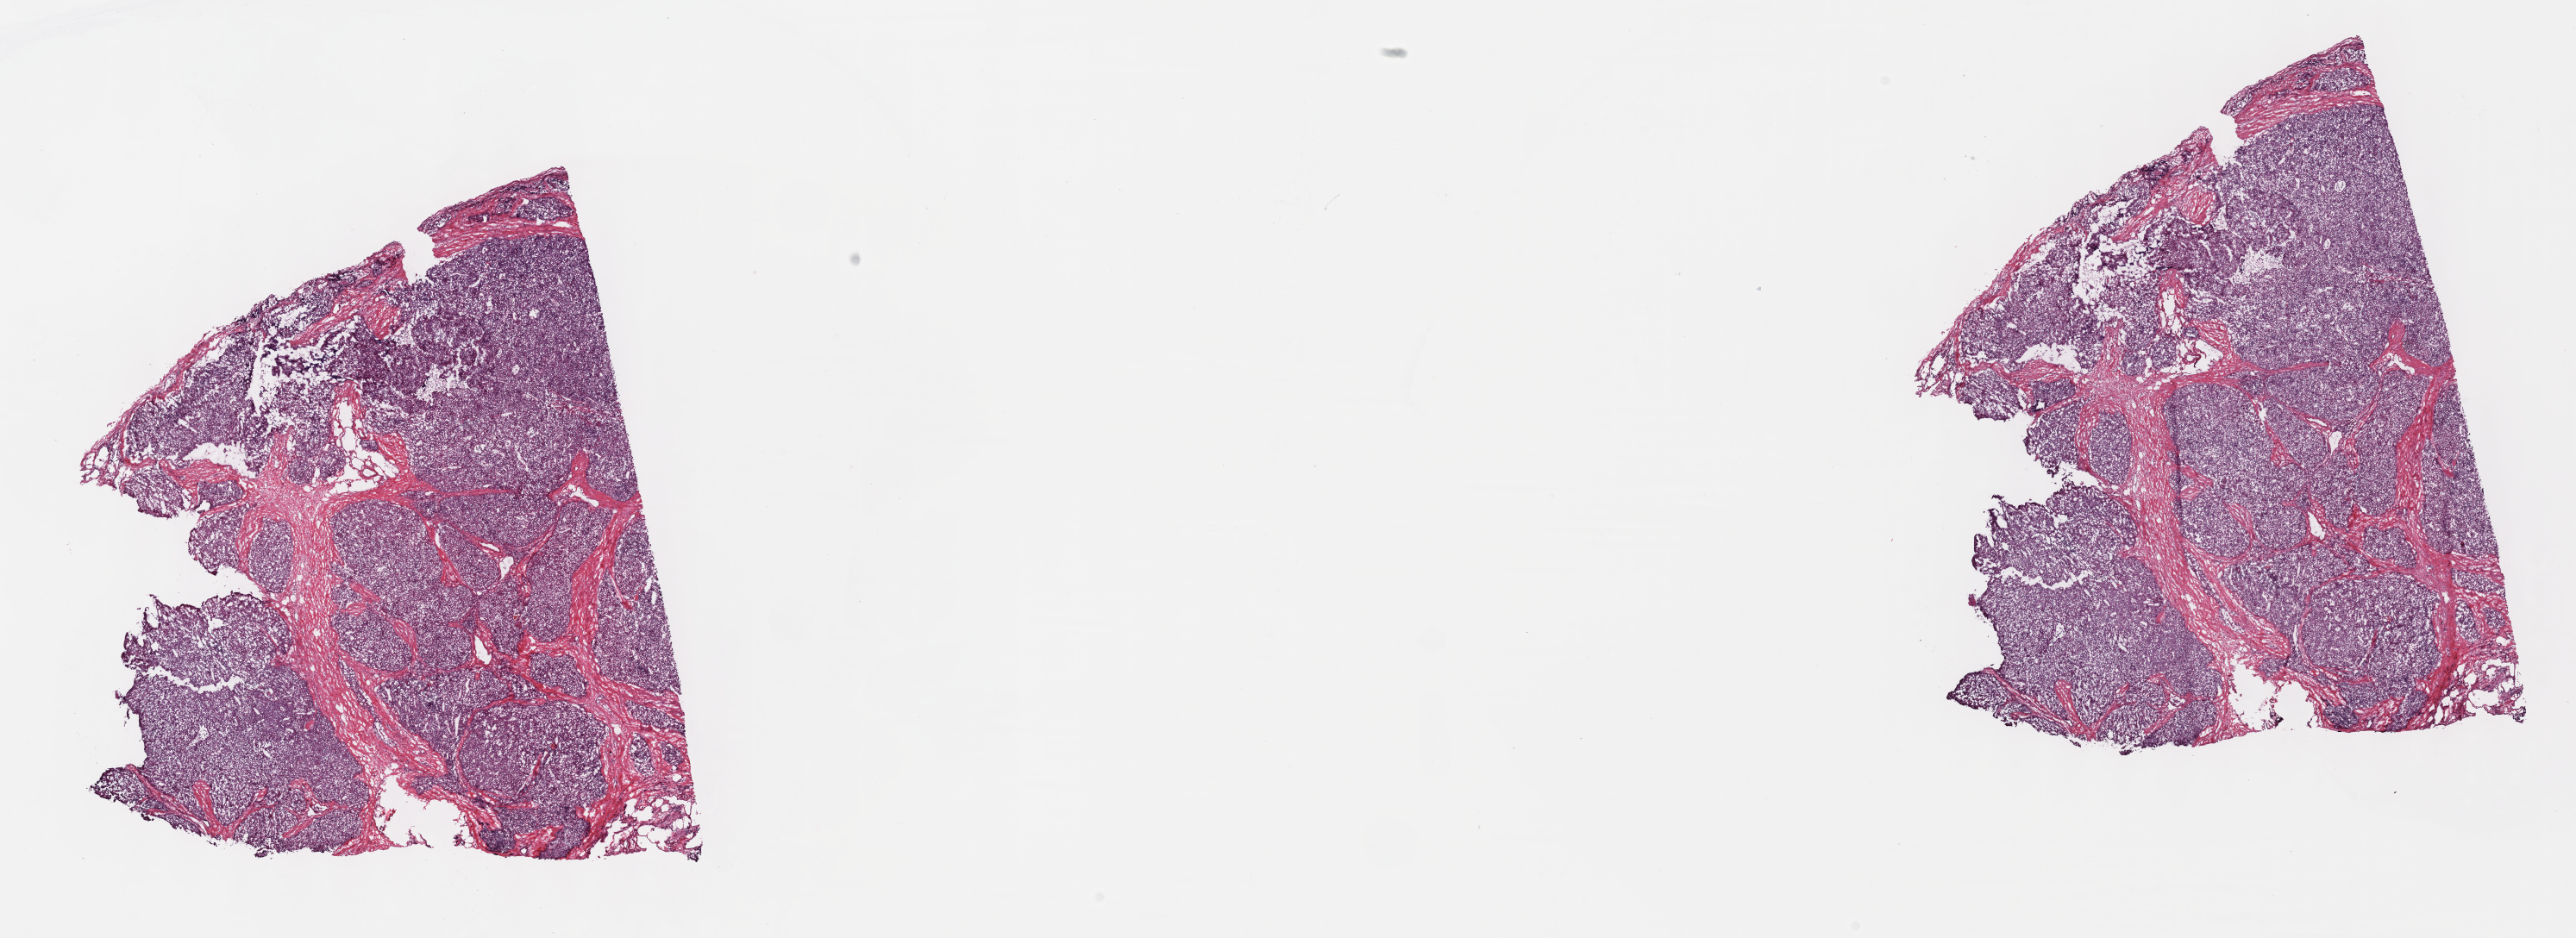
H&E-stained whole-slide image — a low-resolution overview of the entire scanned area, about 24.2 x 8.8 mm (slide scanned at 40x). Frozen section from the top of the tissue portion. Thymus, primary tumour sample. Male, age 62 years at initial diagnosis. Pathologist review of this section (percent, as recorded): tumour cells 95%, tumour nuclei 95%, normal cells 0%, stromal cells 5%, necrosis 0%. Inflammatory infiltration, as recorded: lymphocyte infiltration 0%, monocyte infiltration 0%, neutrophil infiltration 0%.
* diagnosis: Thymoma, type B3, malignant (anterior mediastinum)